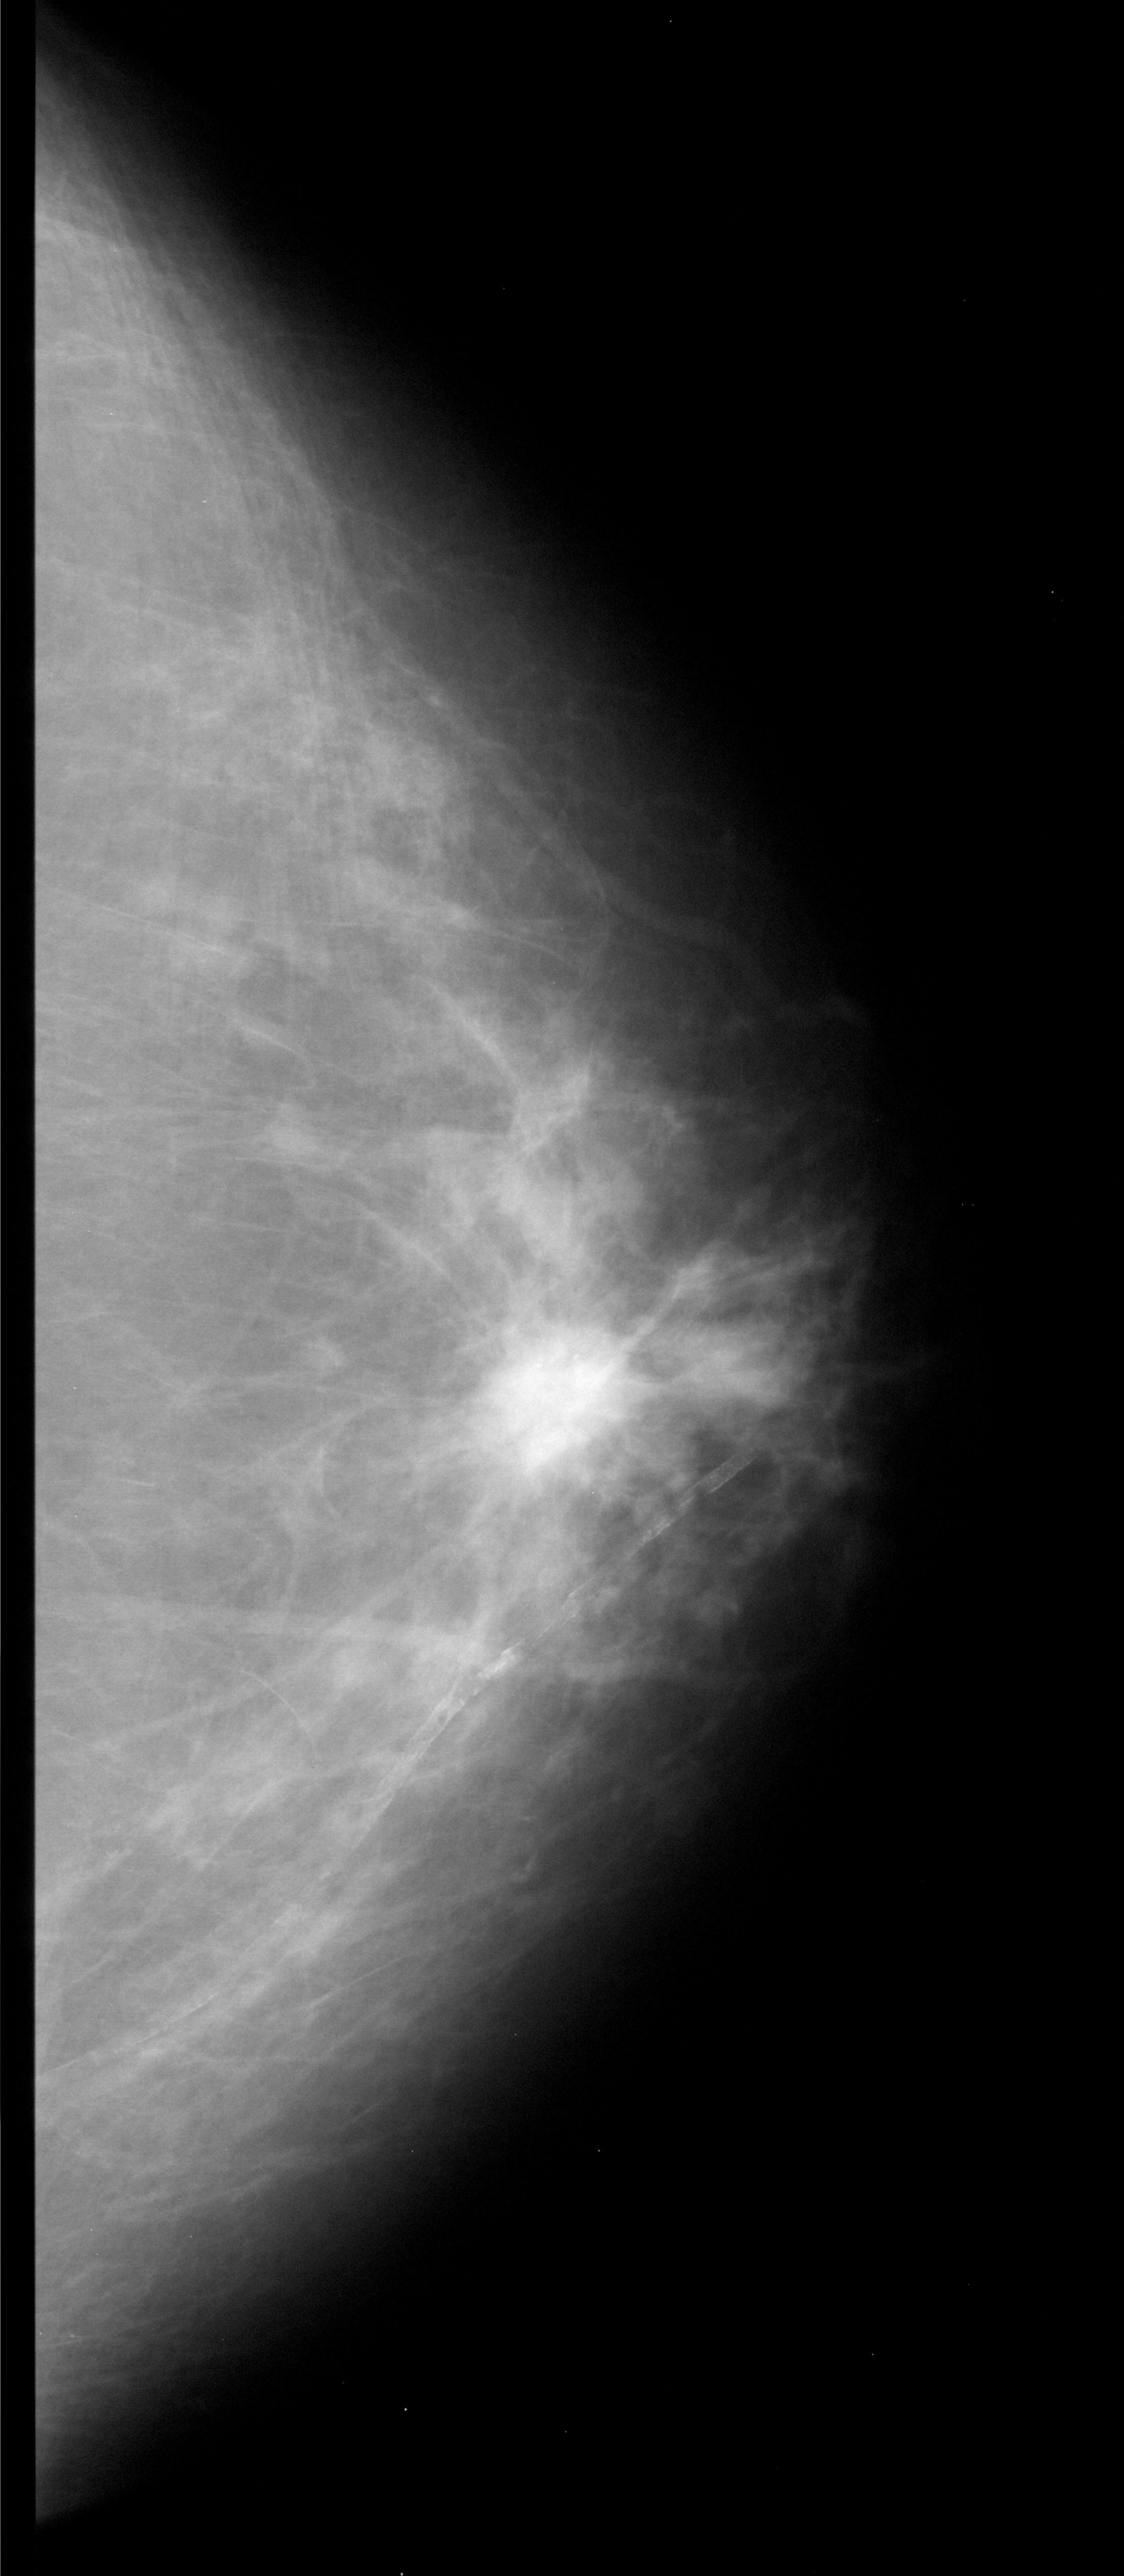
Mammogram (digitized film). Right breast. CC view. BI-RADS breast density category 2 (scale 1–4). 1124 × 2576 image matrix.
Expert-marked regions of interest on this film, with their recorded descriptors:
- mass, shape irregular, margins spiculated; BI-RADS assessment category 5; pathology result (as recorded, not read from the image): malignant: bounding box <468,1284,685,1489> (left, top, right, bottom; pixels)